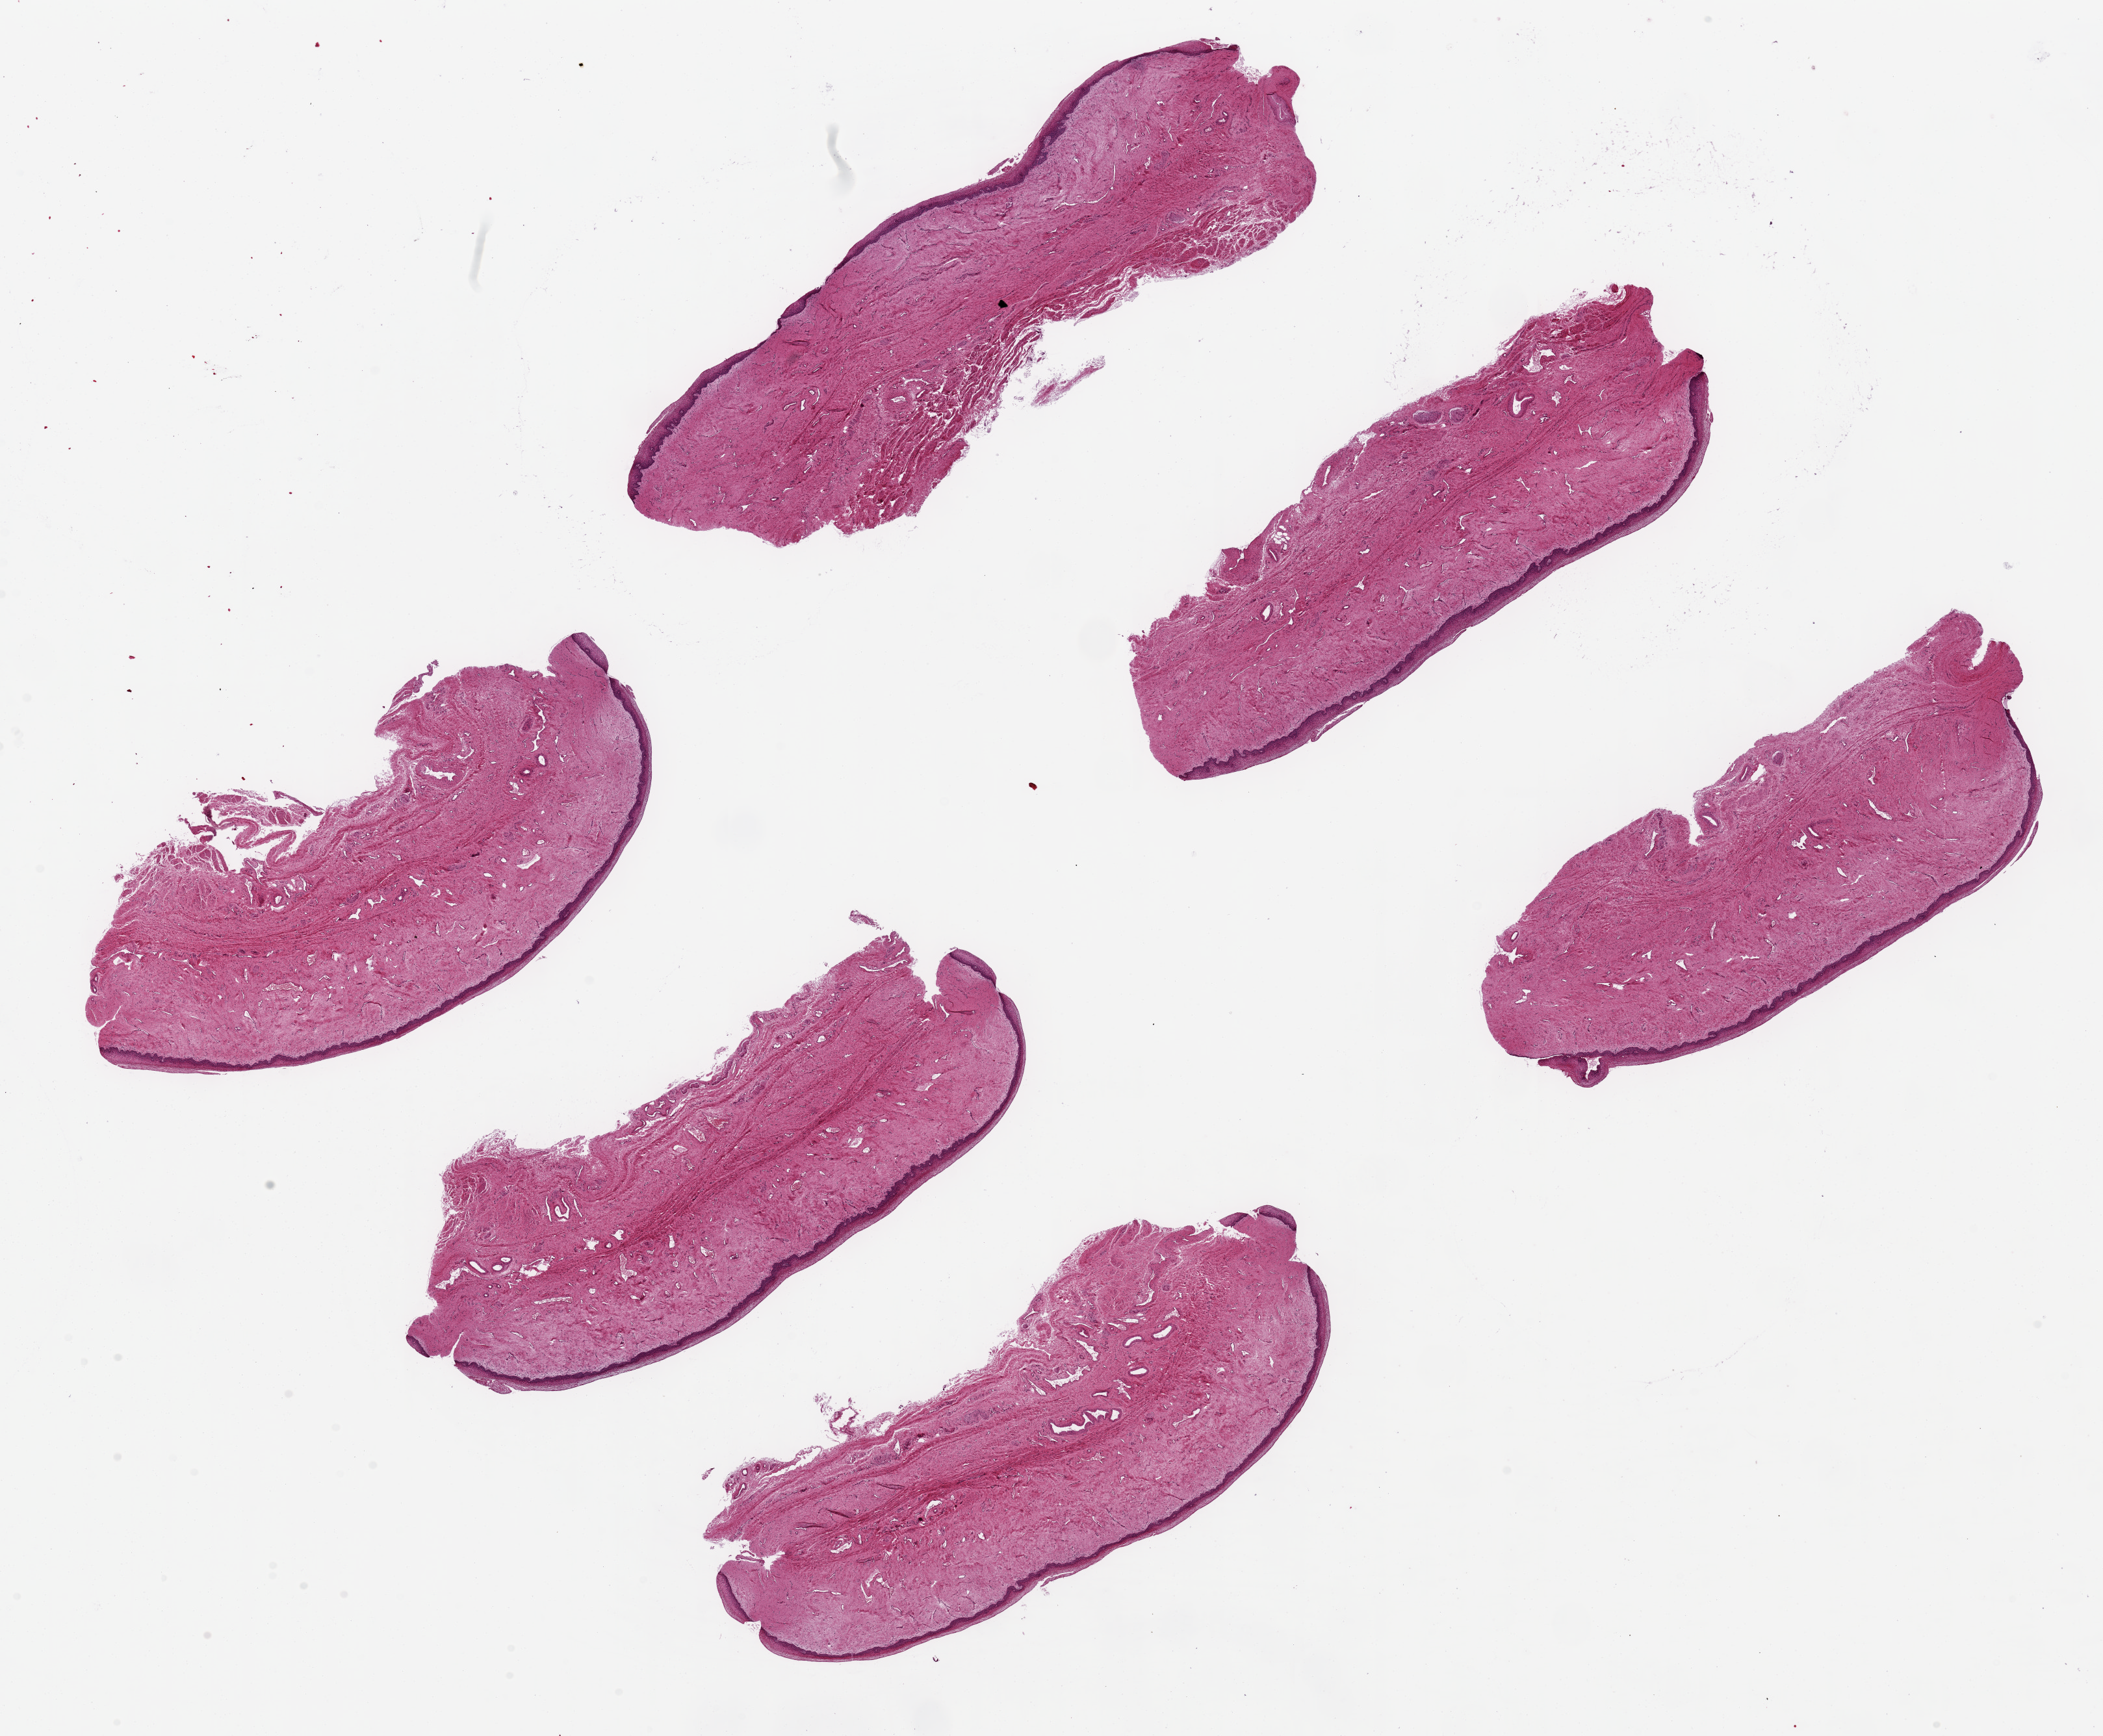
Whole-slide image, haematoxylin and eosin stain, a low-resolution overview of the entire scanned area, about 25.6 x 21.1 mm; PAXgene-fixed, paraffin-embedded tissue; target tissue: vagina; tissue donor sample. Donor: female.
• pathologist's review note for this sample: 6 ~8x2.5mm pieces. Squamous mucosa is ~ 5-7% of thickness